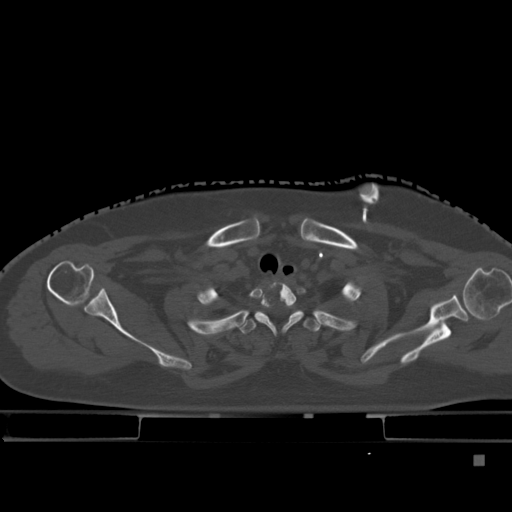
CT including the spine, one axial slice; position 366 of 495 along the scan axis; bone window (W 1800 / L 400 HU); 1.5 mm slice thickness; 512 × 512 image matrix, field of view 404 × 404 mm. Patient: female, 33 years. Case-level facts recorded for this patient, not image findings: primary cancer: breast.
Annotated regions visible in this slice (semi-automatic segmentation, software-assisted and operator-edited):
- T1 vertebra: box from (x=259, y=281) to (x=301, y=332) px
- T2 vertebra: (x=238, y=310)–(x=342, y=334)